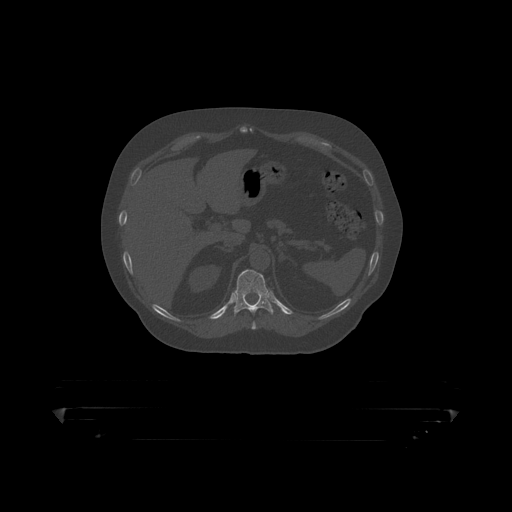
CT including the spine, one axial slice. Position 197 of 390 along the scan axis. Reconstruction kernel STANDARD. 120 kVp. Bone window (W 1800 / L 400 HU). 512 × 512 image matrix, field of view 650 × 650 mm. Male patient, age 60 years. Case-level facts recorded for this patient, not image findings: primary cancer: prostate.
Outlined on this slice (semi-automatic segmentation, software-assisted and operator-edited):
- T11 vertebra: box from (x=226, y=270) to (x=290, y=315) px